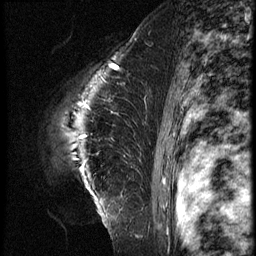
Breast MRI (dynamic contrast-enhanced), one sagittal slice; position 48 of 62 along the scan axis; 3 images stored at this slice position (order not interpretable as contrast timing); 1.5 T; TE 4.2 ms, TR 9 ms; 2.5 mm slice thickness; 256 × 256 image matrix, field of view 180 × 180 mm. Female patient, age 39 years. From the clinical record (not read from this slice): setting: breast cancer imaged before/during neoadjuvant chemotherapy; receptor status: HER2-positive.
Annotated regions visible in this slice (semi-automatically segmented with operator editing):
- analysis volume of interest (the breast-tissue region the enhancement analysis was run in; not a lesion): bounding box <26,64,152,228> (left, top, right, bottom; pixels)
- tumour enhancement mask (voxels above the 140 % enhancement threshold inside the analysis volume of interest): <84,64,120,138>